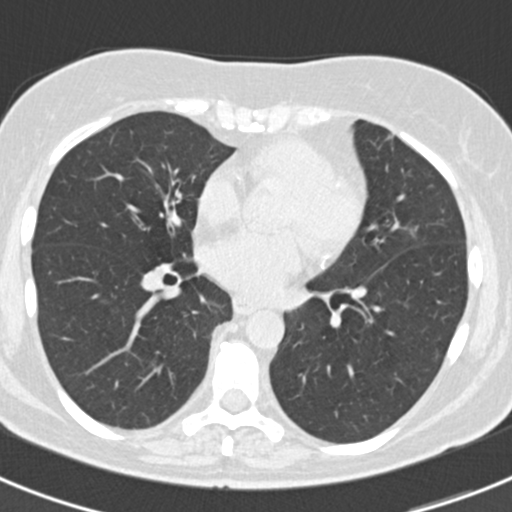
Chest CT (low-dose screening protocol), one axial image. Baseline annual screen. Lung window (W 1500 / L -600 HU). Standard (soft-tissue) reconstruction kernel (B30f). 120 kVp. Female participant, aged 60 years at enrolment. Current smoker at enrolment.
- Expert reader's lesion annotation, bounding box [x1, y1, x2, y2] px = [396, 215, 431, 251].
- The screening reader recorded 3 non-calcified nodules or masses ≥4 mm on this exam (lingula, left lower lobe, lingula); which of them this box marks is not recorded.
- Official screen result: positive, change unspecified: nodule(s) >= 4 mm or enlarging nodule(s), mass(es), or other non-specific abnormalities suspicious for lung cancer.
- Lung cancer was diagnosed 886 days after this screen: non-small cell carcinoma, left upper lobe, poorly differentiated (G3), stage IB (AJCC 6th edition), 7 mm at pathology.